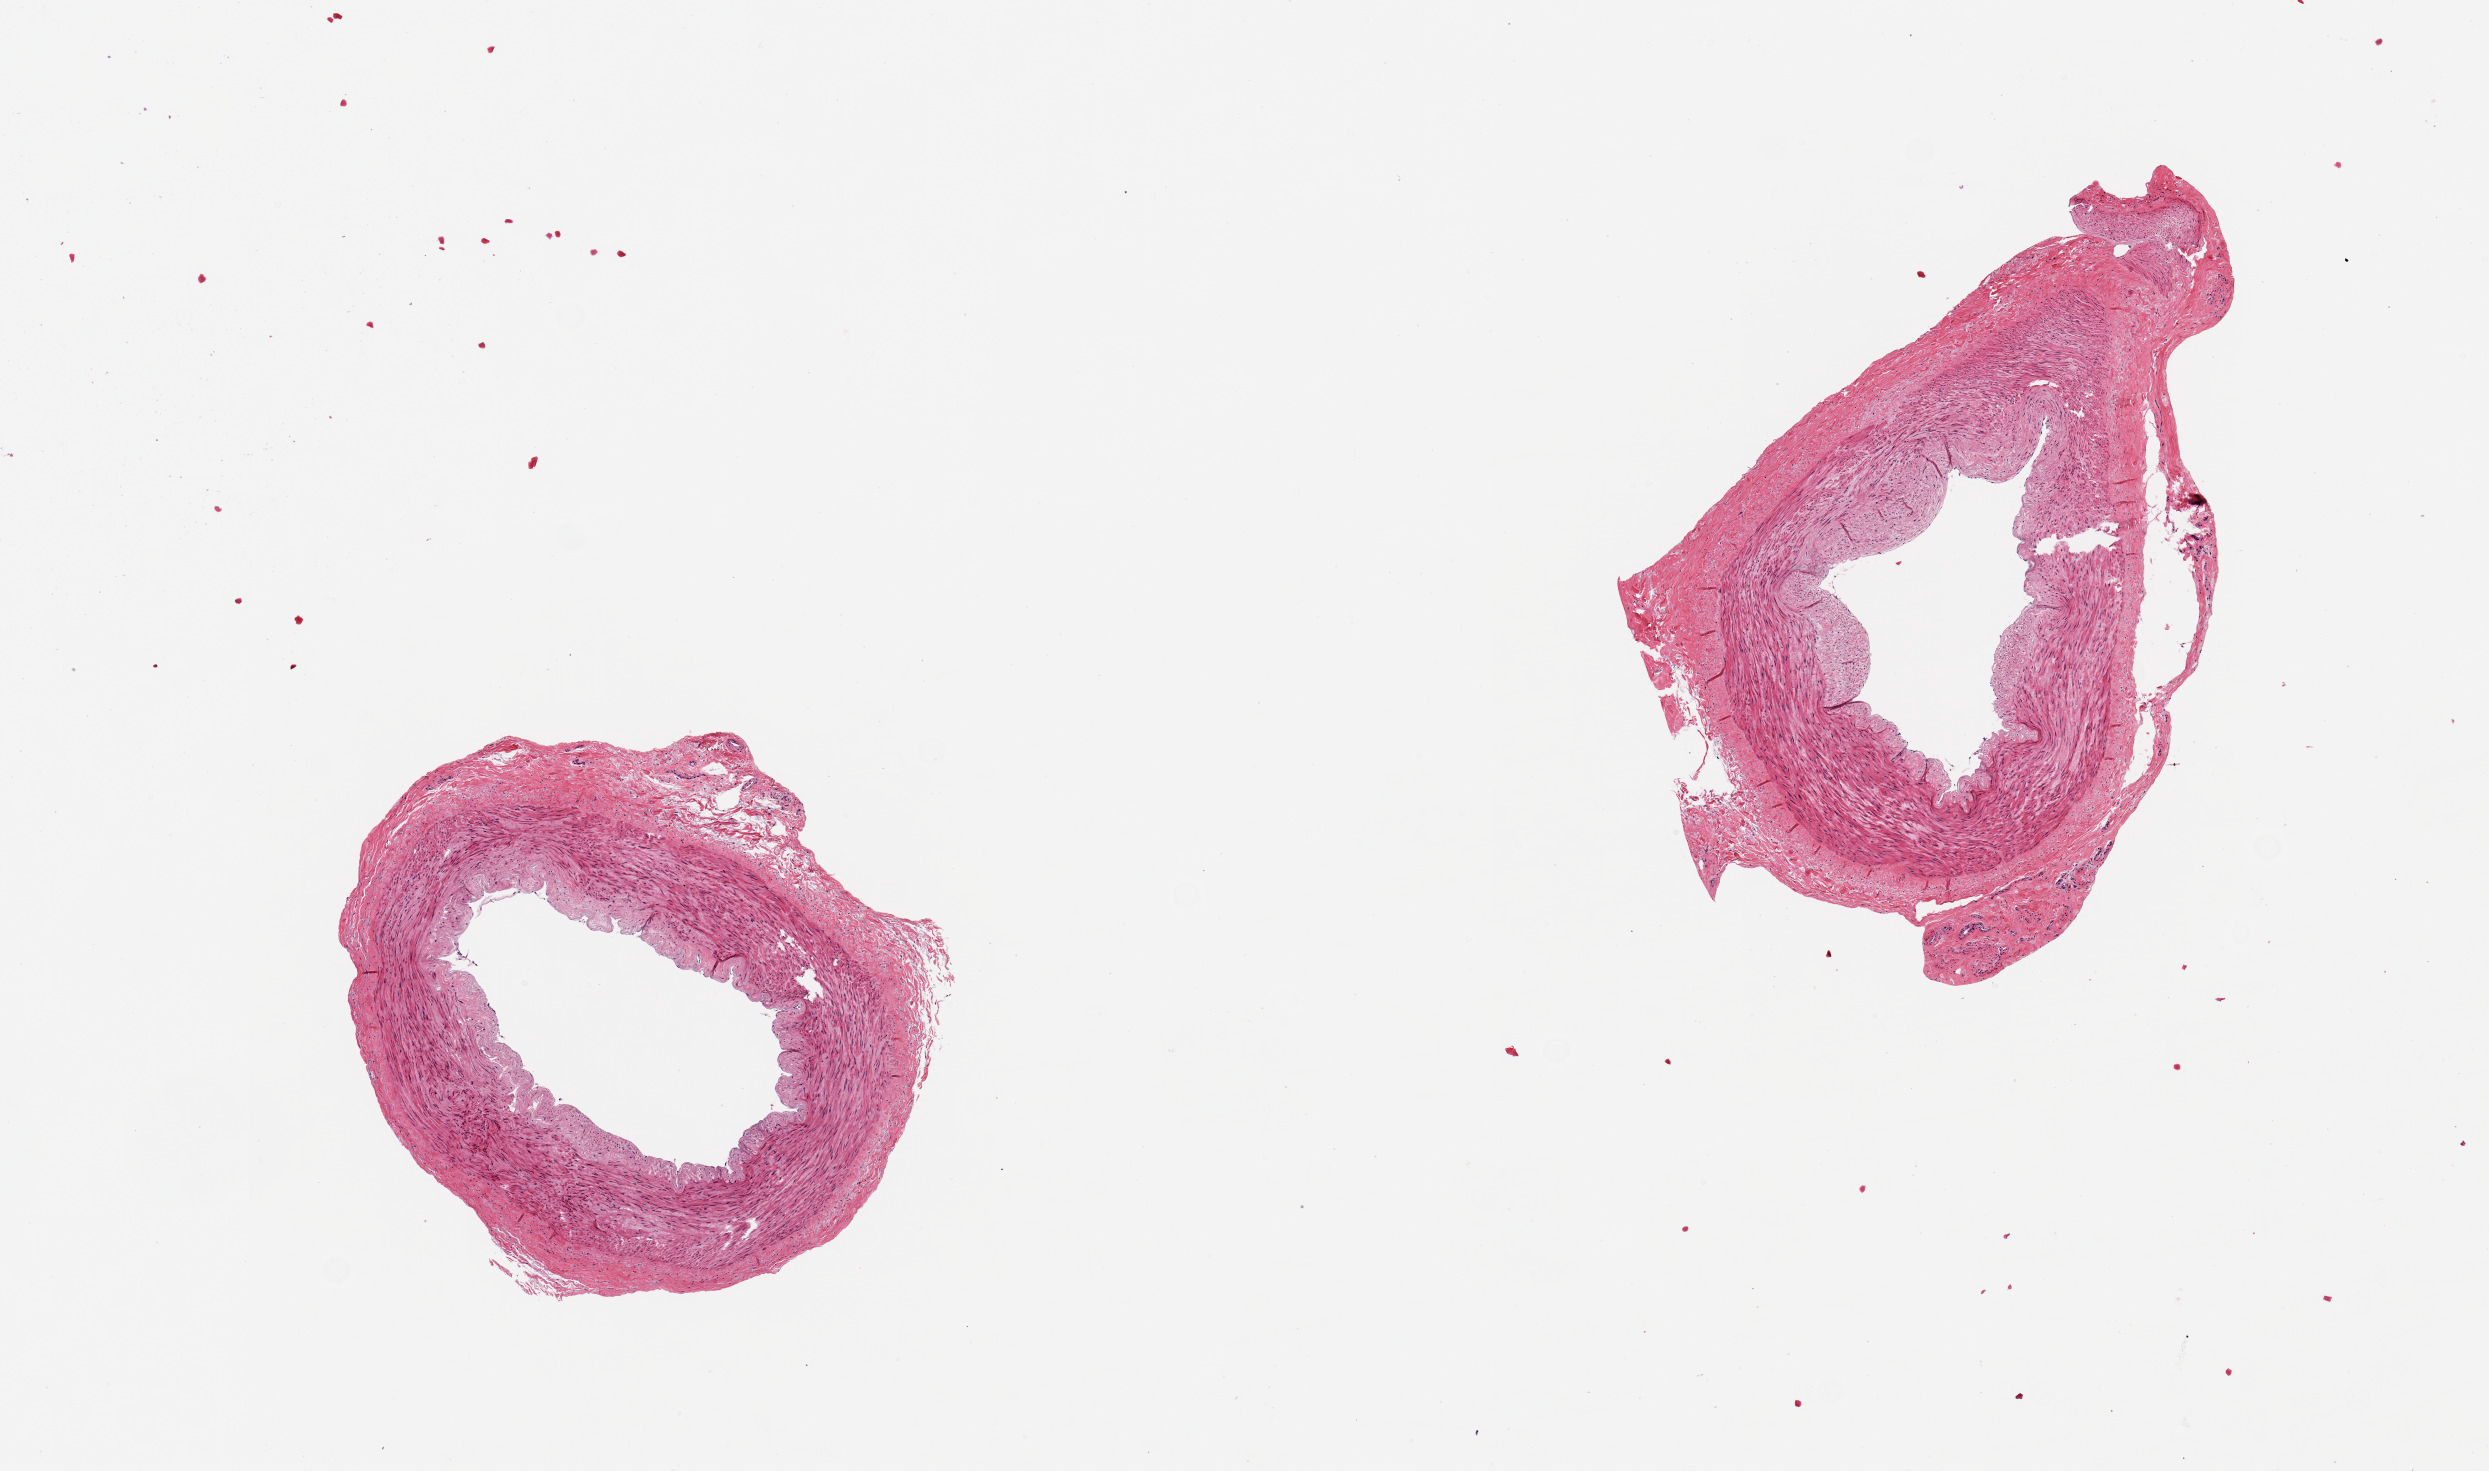
Digitized haematoxylin and eosin-stained section — shown as a low-resolution overview of the whole scanned area (about 9.8 x 5.8 mm, from a 20x scan); PAXgene-fixed, paraffin-embedded tissue; target tissue: tibial artery; tissue donor sample. Donor: female.
Review note (as recorded): 2 pieces 2 mm arteries with no abnormalities.